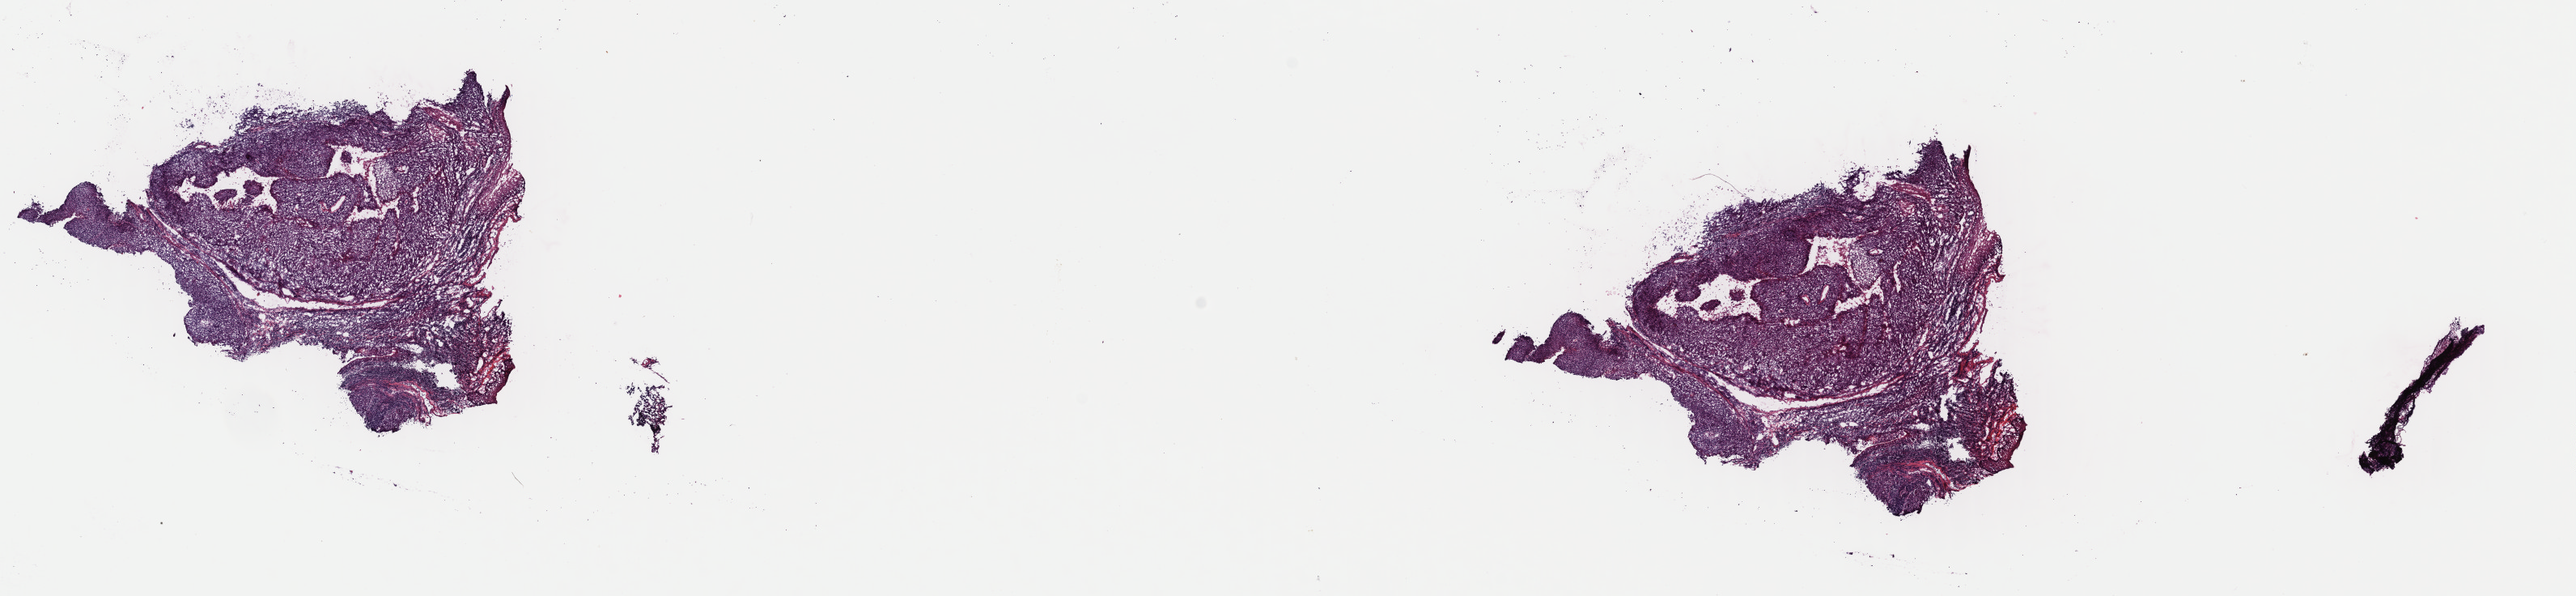
Whole-slide histology image, H&E-stained, low-resolution overview of the scanned area, about 25.1 x 5.8 mm (slide scanned at 40x); frozen section; primary tumour sample from the head and neck. Male patient; age at initial diagnosis 56 years. Histologic grade: G2 (moderately differentiated). Pathologist review of this section (percent, as recorded): tumour cells 75%, tumour nuclei 75%, normal cells 20%, stromal cells 5%, necrosis 0%. Inflammatory infiltration, as recorded: lymphocyte infiltration 20%, monocyte infiltration 0%, neutrophil infiltration 0%.
• AJCC pathologic stage: II (7th edition)
• histologic diagnosis: Squamous cell carcinoma, NOS